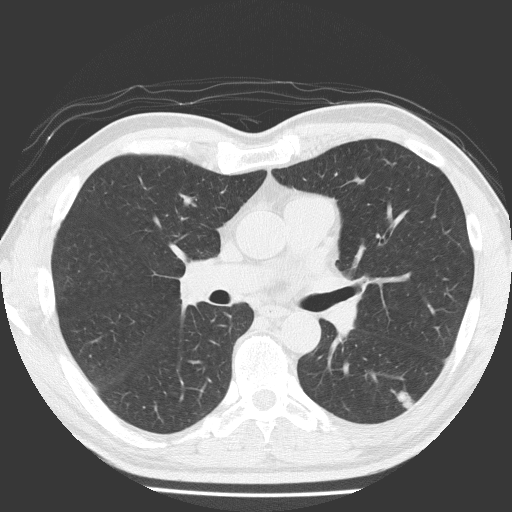
Low-dose screening chest CT, one axial slice; slice 104 of 184 in the series (ordered by position); 120 kVp; lung window (W 1500 / L -600 HU); 512 × 512 image matrix, field of view 348 × 348 mm.
Annotated regions visible in this slice (expert manual segmentation):
- lesion 1 (tumor, lower lobe of left lung): box from (x=392, y=390) to (x=414, y=409) px